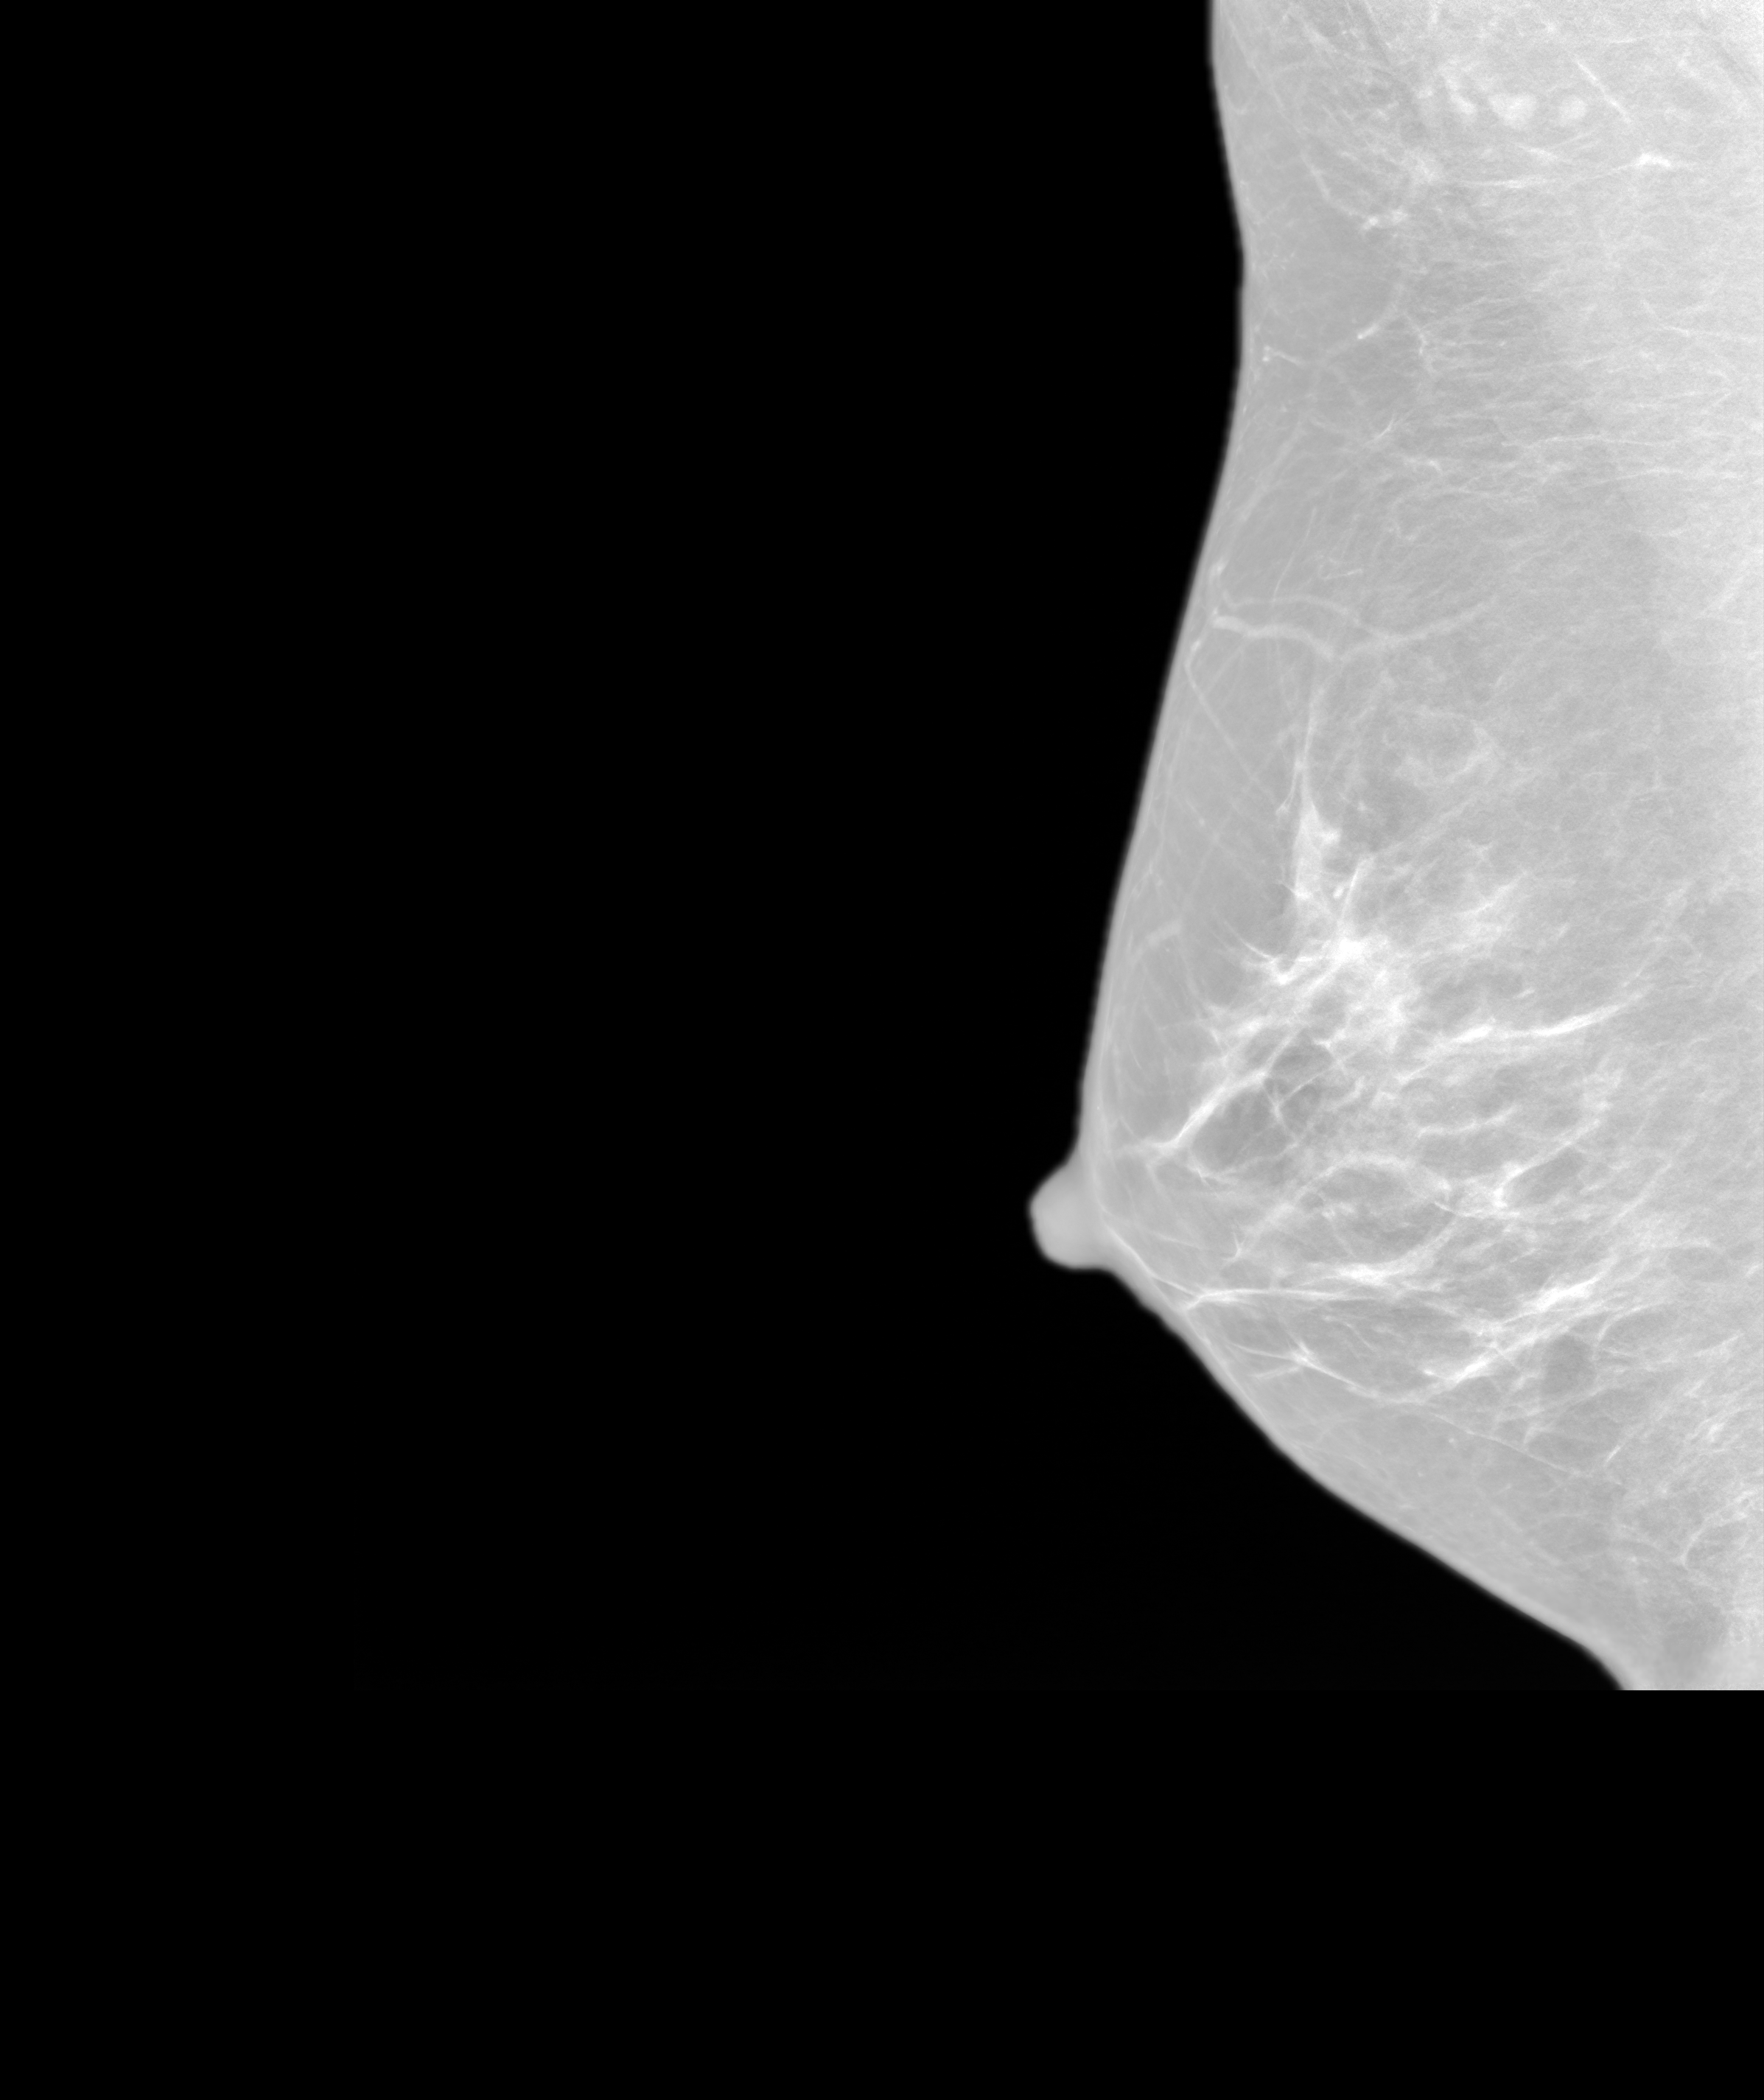
Synthesized 2-D mammogram reconstructed from digital breast tomosynthesis, right breast, MLO view, annual screening mammography examination, system: SenoIris_1SP1.1(421). Female patient, age 43 years.
Breast density at the screening exam (both breasts): scattered fibroglandular densities (BI-RADS density category b). Final BI-RADS assessment for this screening round (tomosynthesis exam, both breasts): category 1. Recall: no recall after this screen.